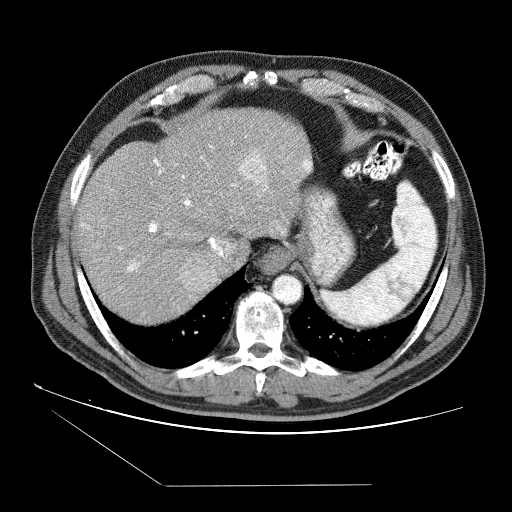
Contrast-enhanced abdominal CT (liver protocol), one axial slice; slice 66 of 87 in the series (ordered by position); soft-tissue window (W 400 / L 40 HU); 2.5 mm slice thickness; 512 × 512 image matrix, field of view 400 × 400 mm. Case-level facts recorded for this patient, not image findings: diagnosis: hepatocellular carcinoma (patient treated with transarterial chemoembolisation; whether this scan precedes or follows treatment is not stated here); TNM stage (as recorded): Stage-II; Child-Pugh class: B; tumour differentiation: no biopsy; tumour nodularity: multinodular.
Structures marked on this image (semi-automatically segmented with operator editing):
- abdominal aorta: bounding box (x1, y1, x2, y2) in pixels: (273, 275, 301, 303)
- liver parenchyma outside the tumour (the mass and vessels are separate outlines, so this box may not span the whole liver): (76, 108, 310, 323)
- mass: (178, 156, 266, 296)
- liver vessels: (81, 141, 308, 297)